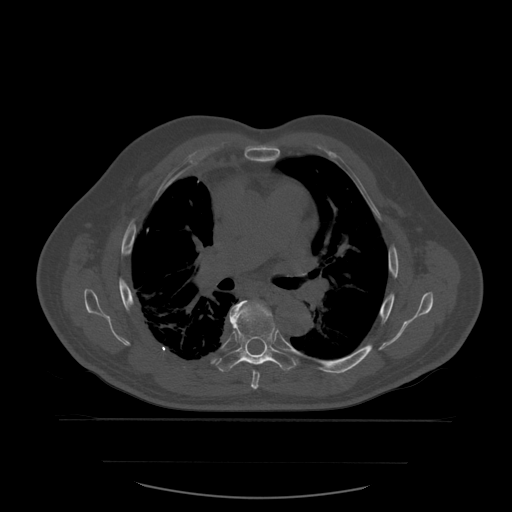
CT including the spine, one axial slice. Slice 390 of 590 in the series (ordered by position). Bone window (W 1800 / L 400 HU). 512 × 512 image matrix, field of view 479 × 479 mm. Patient age 71 years. From the clinical record (not read from this slice): primary cancer: lung; vertebrae with lytic lesions (as recorded): T1, T2, L5, S1.
Annotated regions visible in this slice (semi-automatic segmentation, software-assisted and operator-edited):
- T6 vertebra: bounding box [x1, y1, x2, y2] px = [241, 301, 267, 390]
- T7 vertebra: [216, 301, 297, 372]